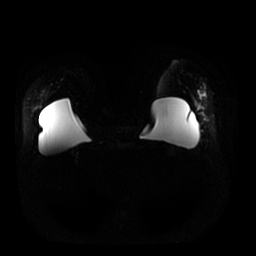
Breast MRI, one axial slice. Diffusion-weighted series; image 2 of 4 stored at this slice position (different b-values; order by instance number). 1.5 T. 4 mm slice thickness. 256 × 256 image matrix, field of view 380 × 380 mm. Female patient.
Structures marked on this image (manually delineated by an expert):
- tumour on diffusion-weighted imaging: bounding box [x1, y1, x2, y2] px = [201, 97, 207, 107]